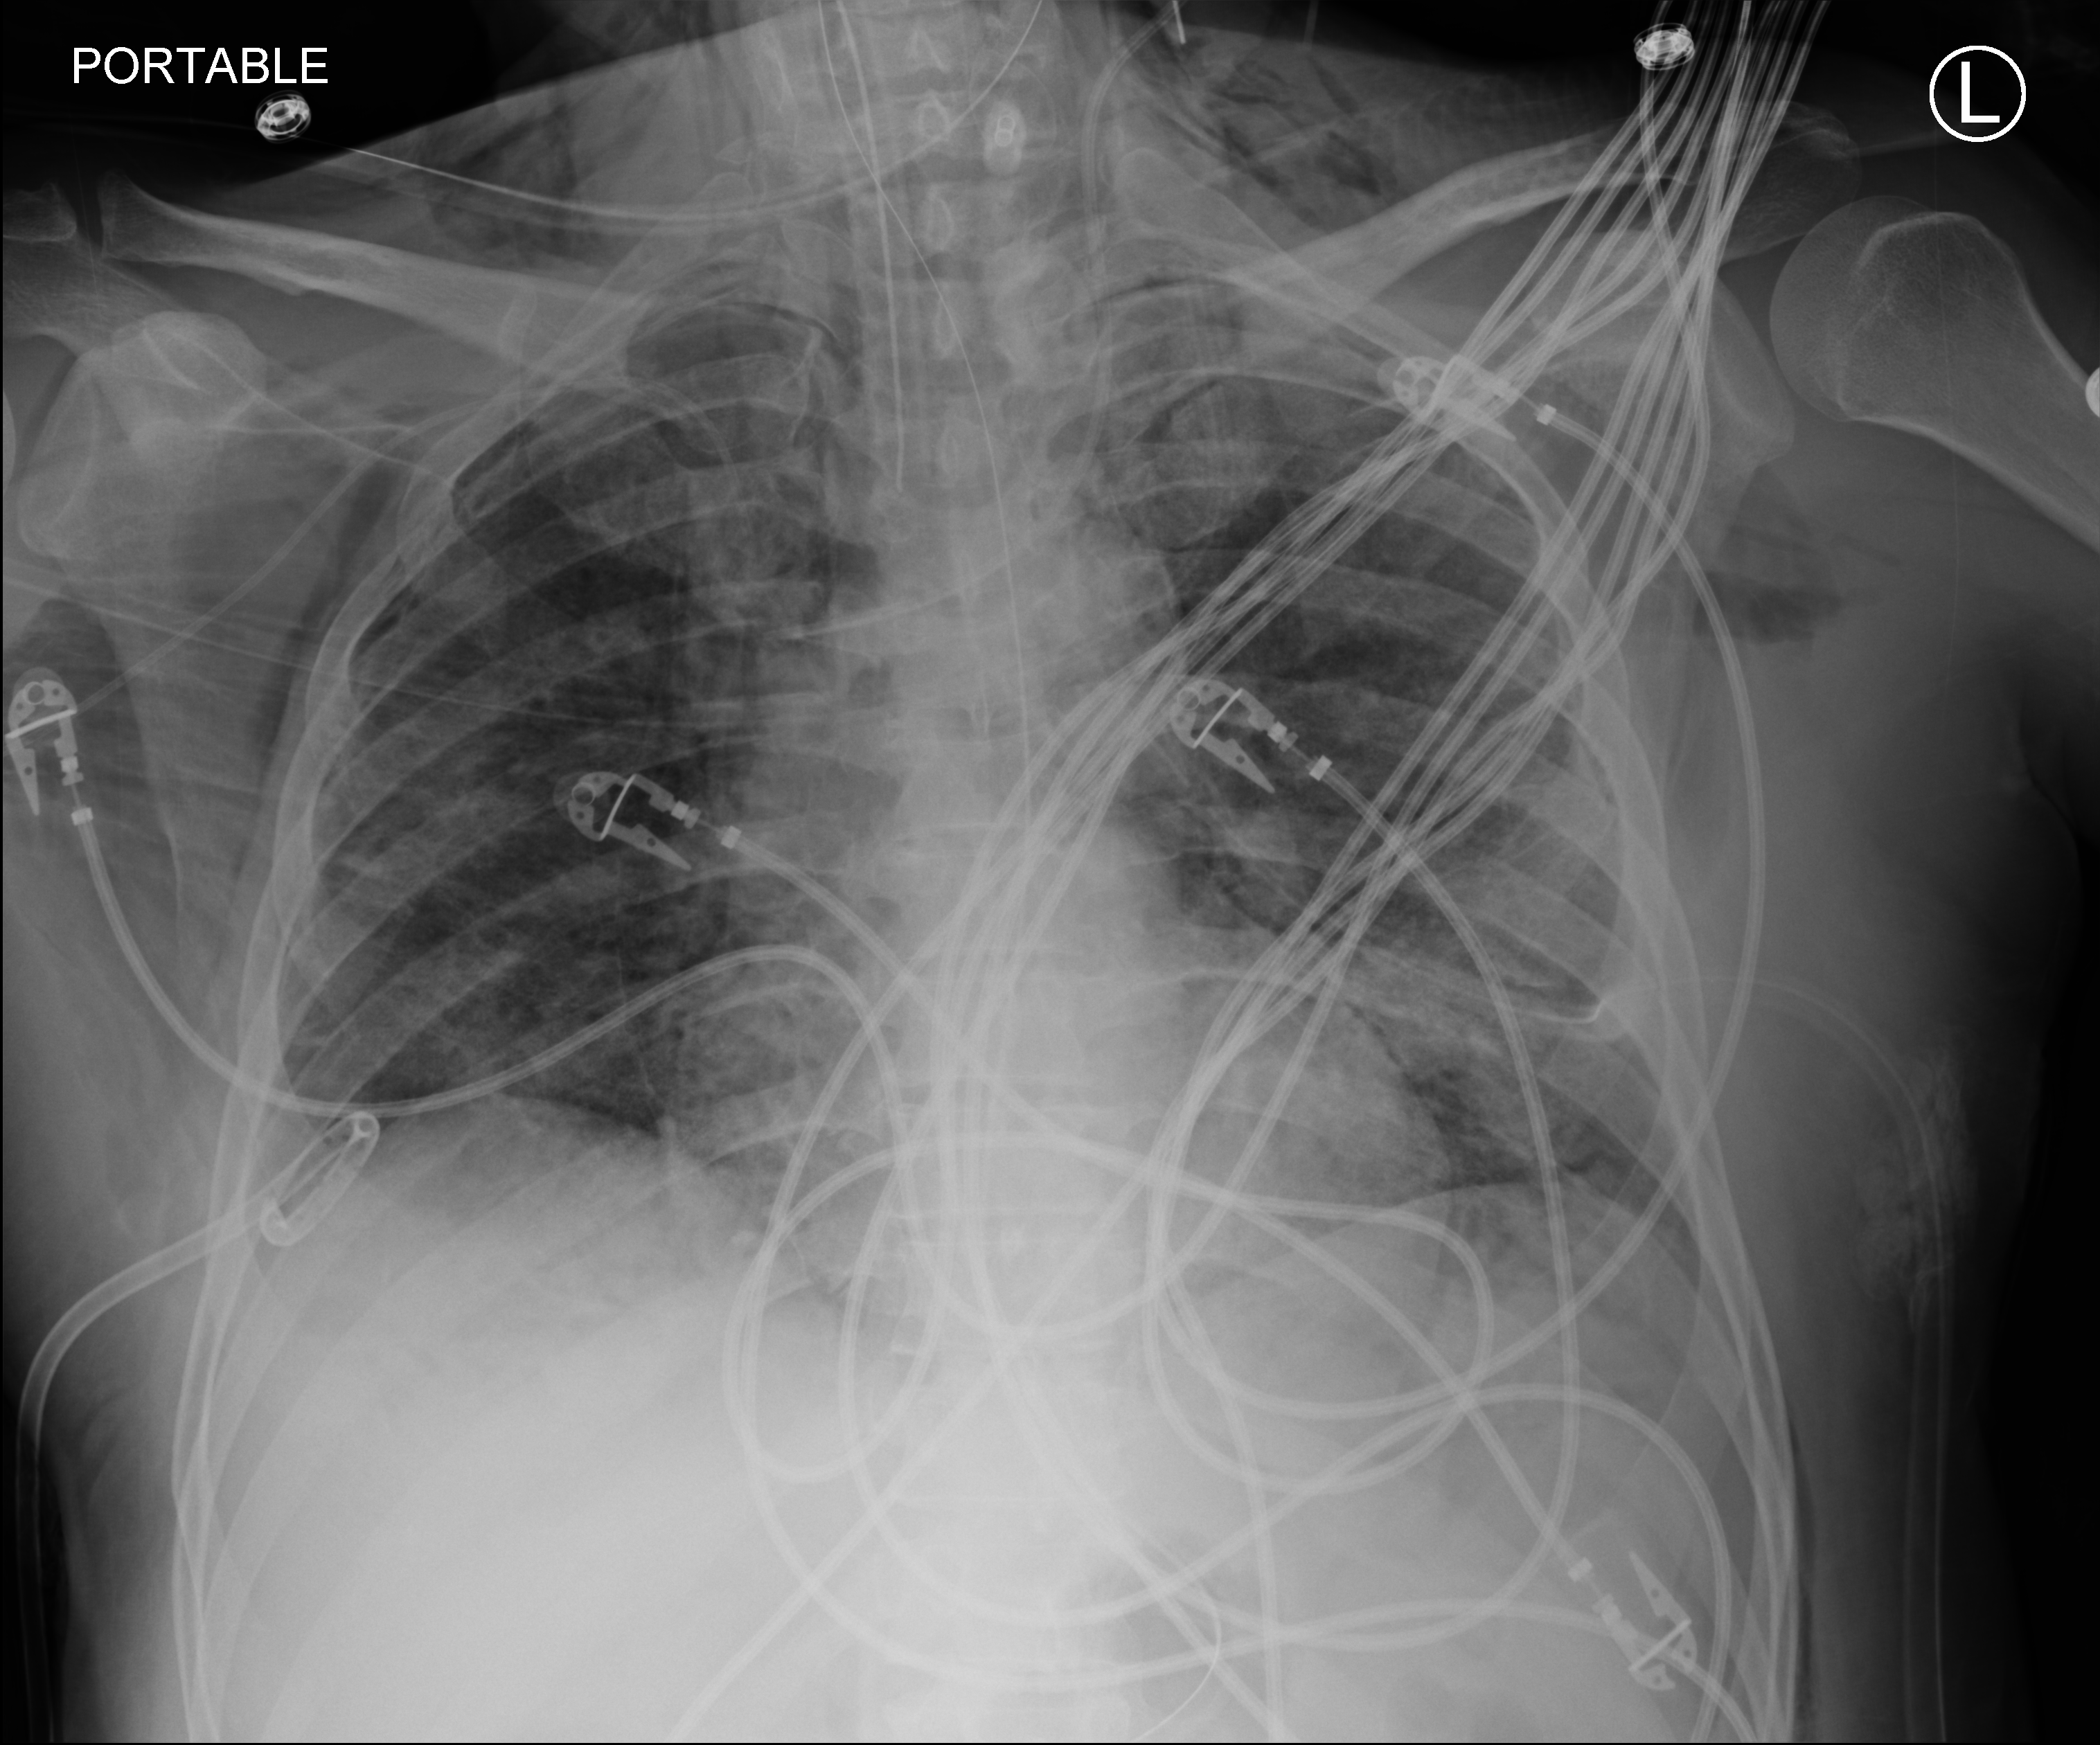
Bedside chest radiograph (computed radiography). Patient hospitalised with COVID-19; male, aged 18–59 years.
Admission-level facts for this patient (not findings on this image; timing relative to this image not recorded):
- mechanically ventilated during this hospital stay: yes
- smoking status (admission record): never